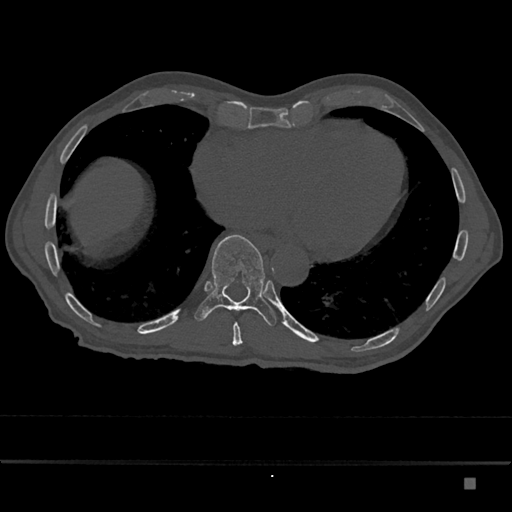
CT including the spine, one axial slice; slice 755 of 797 in the series (ordered by position); bone window (W 1800 / L 400 HU); 0.5 mm slice thickness; 512 × 512 image matrix, field of view 390 × 390 mm. Male patient, age 72 years. From the clinical record (not read from this slice): primary cancer: prostate.
Structures marked on this image (semi-automatic segmentation, software-assisted and operator-edited):
- T10 vertebra: bounding box [x1, y1, x2, y2] px = [194, 234, 277, 326]
- T9 vertebra: [232, 323, 243, 346]